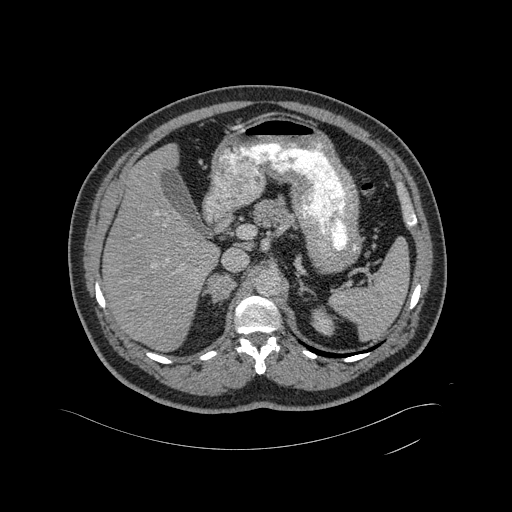
Contrast-enhanced abdominal CT, one axial slice. Position 318 of 433 along the scan axis. 120 kVp. Intravenous contrast given. Soft-tissue window (W 400 / L 40 HU). 2 mm slice thickness. 512 × 512 image matrix, field of view 500 × 500 mm. Patient: male, 56 years. From the clinical record (not read from this slice): diagnosis: adrenocortical carcinoma; tumour side: right adrenal; tumour size at pathology: 11.6 cm; Ki-67 index: 50 %; stage (as recorded): 3.
Annotated regions visible in this slice (semi-automatically segmented with operator editing):
- mass: bounding box [x1, y1, x2, y2] px = [208, 274, 235, 302]